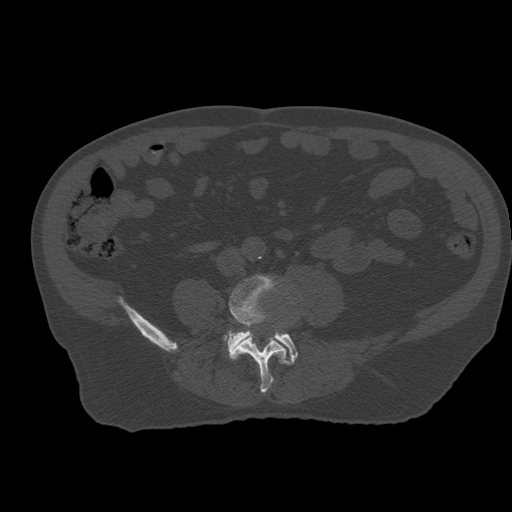
CT including the spine, one axial slice; slice 156 of 399 in the series (ordered by position); reconstruction kernel STANDARD; 120 kVp; bone window (W 1800 / L 400 HU); 1.25 mm slice thickness; 512 × 512 image matrix, field of view 407 × 407 mm. Patient age 73 years. Case-level facts recorded for this patient, not image findings: primary cancer: prostate; vertebrae with lytic lesions (as recorded): L2.
Outlined on this slice (semi-automatically segmented with operator editing):
- L4 vertebra: box from (x=224, y=276) to (x=287, y=394) px
- L5 vertebra: (x=228, y=330)–(x=298, y=365)